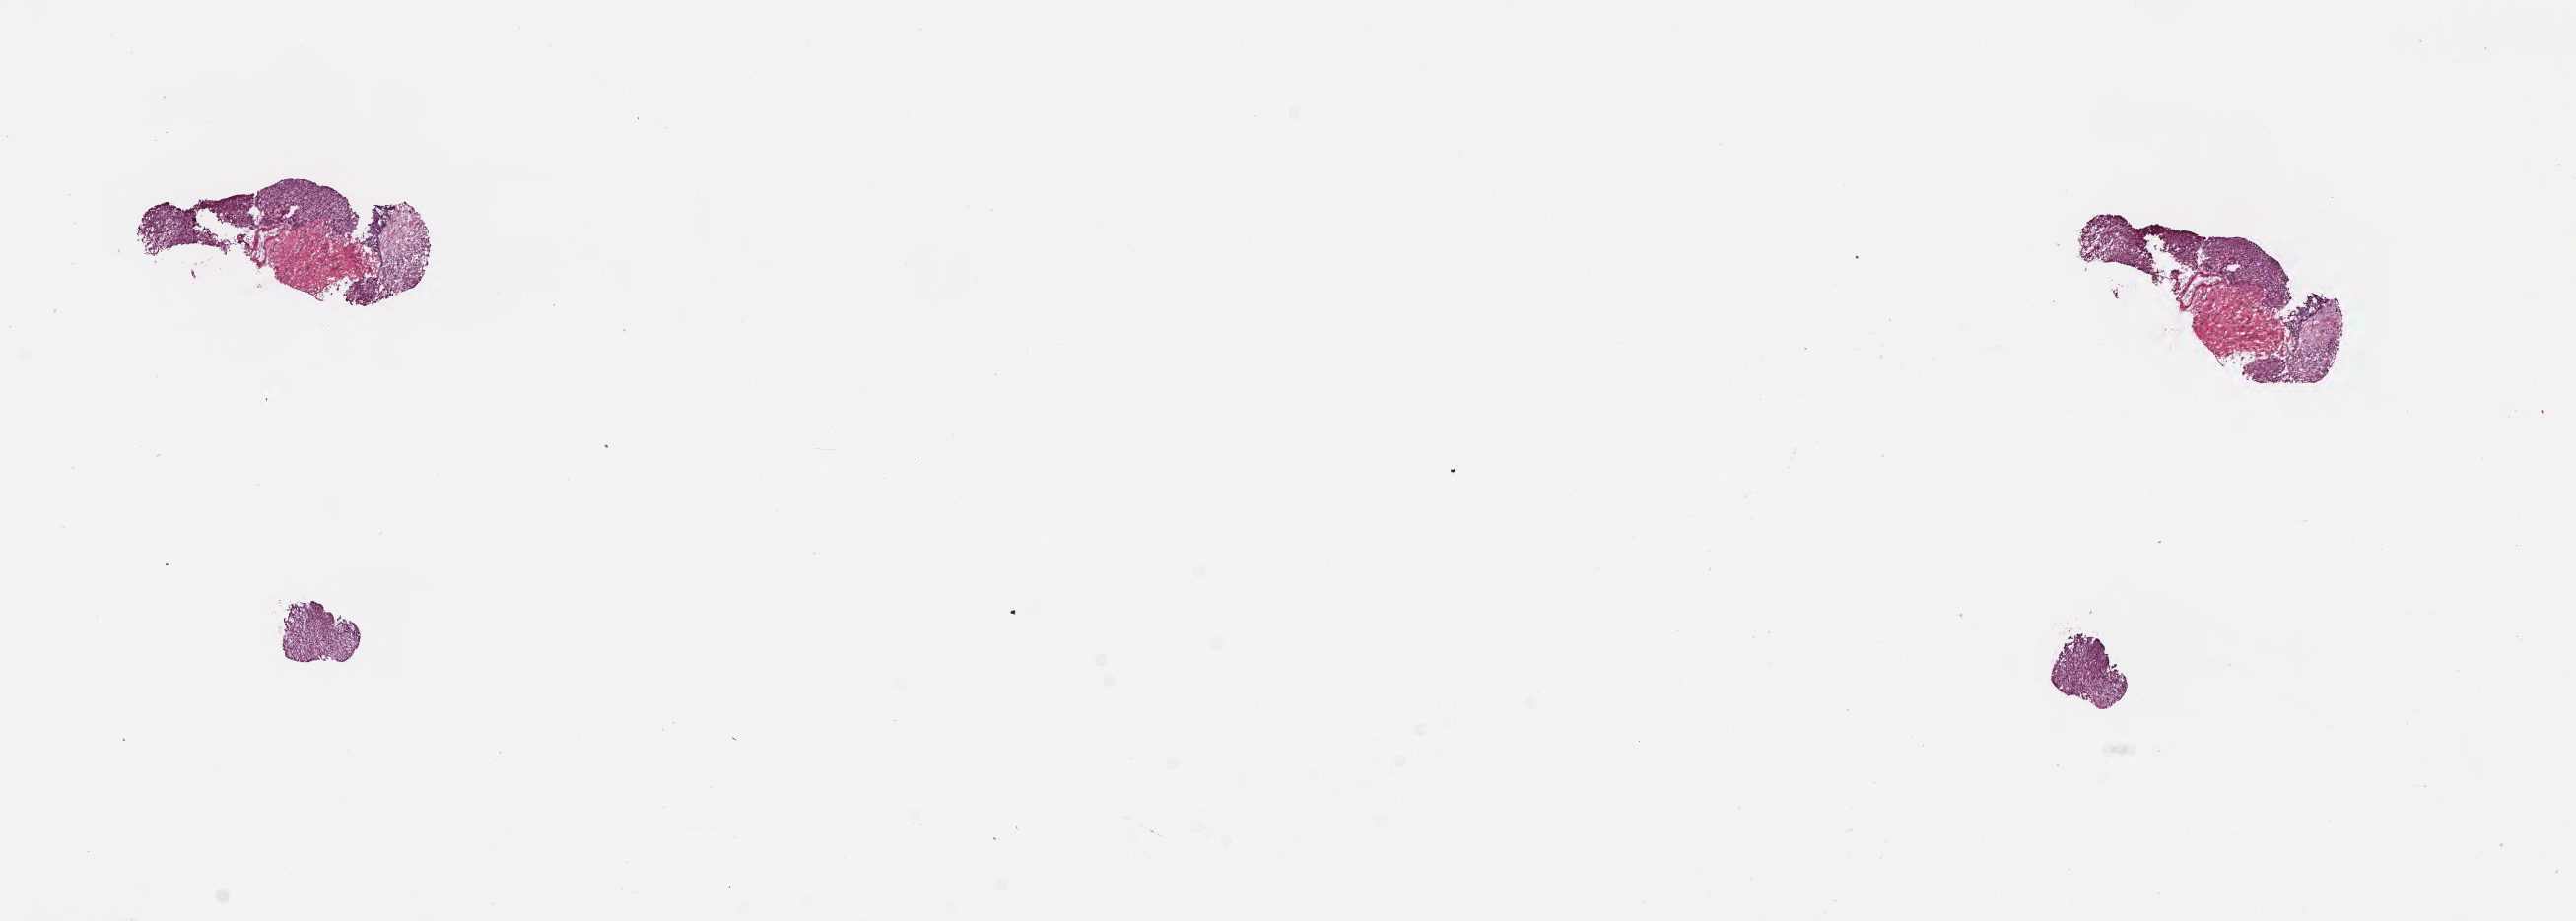
Haematoxylin and eosin whole-slide image, a low-resolution overview of the entire scanned area, about 21.1 x 7.6 mm, frozen section, metastatic tumor tissue, resected from liver. Male, age 63 years at initial diagnosis. Slide review estimates, as recorded: tumor cells 63%, tumor nuclei 88%, stromal cells 27%, necrosis 1%, normal cells 9%. Infiltration values recorded for this section: lymphocyte infiltration 2%, monocyte infiltration 1%, neutrophil infiltration 0%.
Section: top of the tissue portion. Patient diagnosis (primary): Adenocarcinoma, metastatic, NOS.